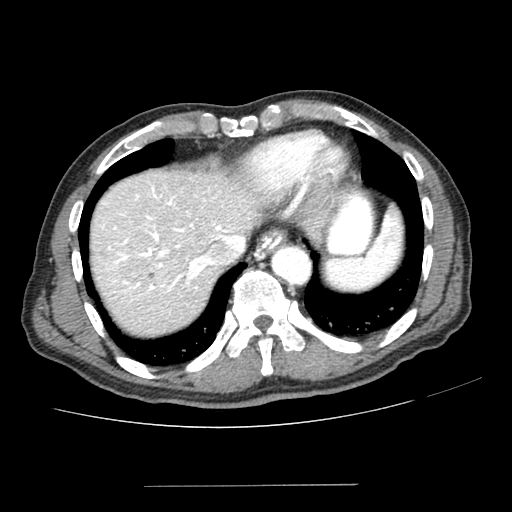
Contrast-enhanced abdominal CT (liver protocol), one axial slice. Slice 173 of 187 in the series (ordered by position). One of 2 acquisitions stored at this slice position. Soft-tissue window (W 400 / L 40 HU). 2.5 mm slice thickness. 512 × 512 image matrix, field of view 360 × 360 mm. From the clinical record (not read from this slice): diagnosis: hepatocellular carcinoma (patient treated with transarterial chemoembolisation; whether this scan precedes or follows treatment is not stated here); TNM stage (as recorded): Stage-I; Child-Pugh class: A; tumour differentiation: poorly differentiated; tumour nodularity: uninodular.
Outlined on this slice (semi-automatically segmented with operator editing):
- abdominal aorta: box from (x=271, y=246) to (x=310, y=284) px
- liver parenchyma outside the tumour (the mass and vessels are separate outlines, so this box may not span the whole liver): (x=90, y=170)–(x=260, y=336)
- mass: (x=119, y=253)–(x=157, y=289)
- liver vessels: (x=101, y=186)–(x=239, y=296)